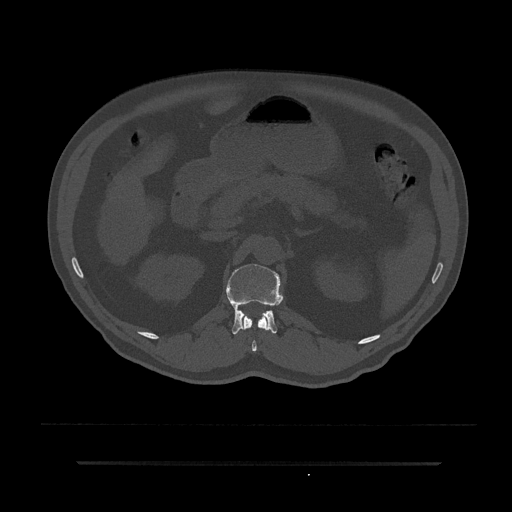
CT including the spine, one axial slice. Slice 172 of 797 in the series (ordered by position). Reconstruction kernel Br40s/3. 120 kVp. Bone window (W 1800 / L 400 HU). 0.5 mm slice thickness. 512 × 512 image matrix. Male patient, age 59 years. From the clinical record (not read from this slice): primary cancer: bile ducts; vertebrae with lytic lesions (as recorded): T10.
Structures marked on this image (semi-automatically segmented with operator editing):
- L1 vertebra: box from (x=226, y=264) to (x=283, y=334) px
- T12 vertebra: (x=240, y=315)–(x=268, y=352)